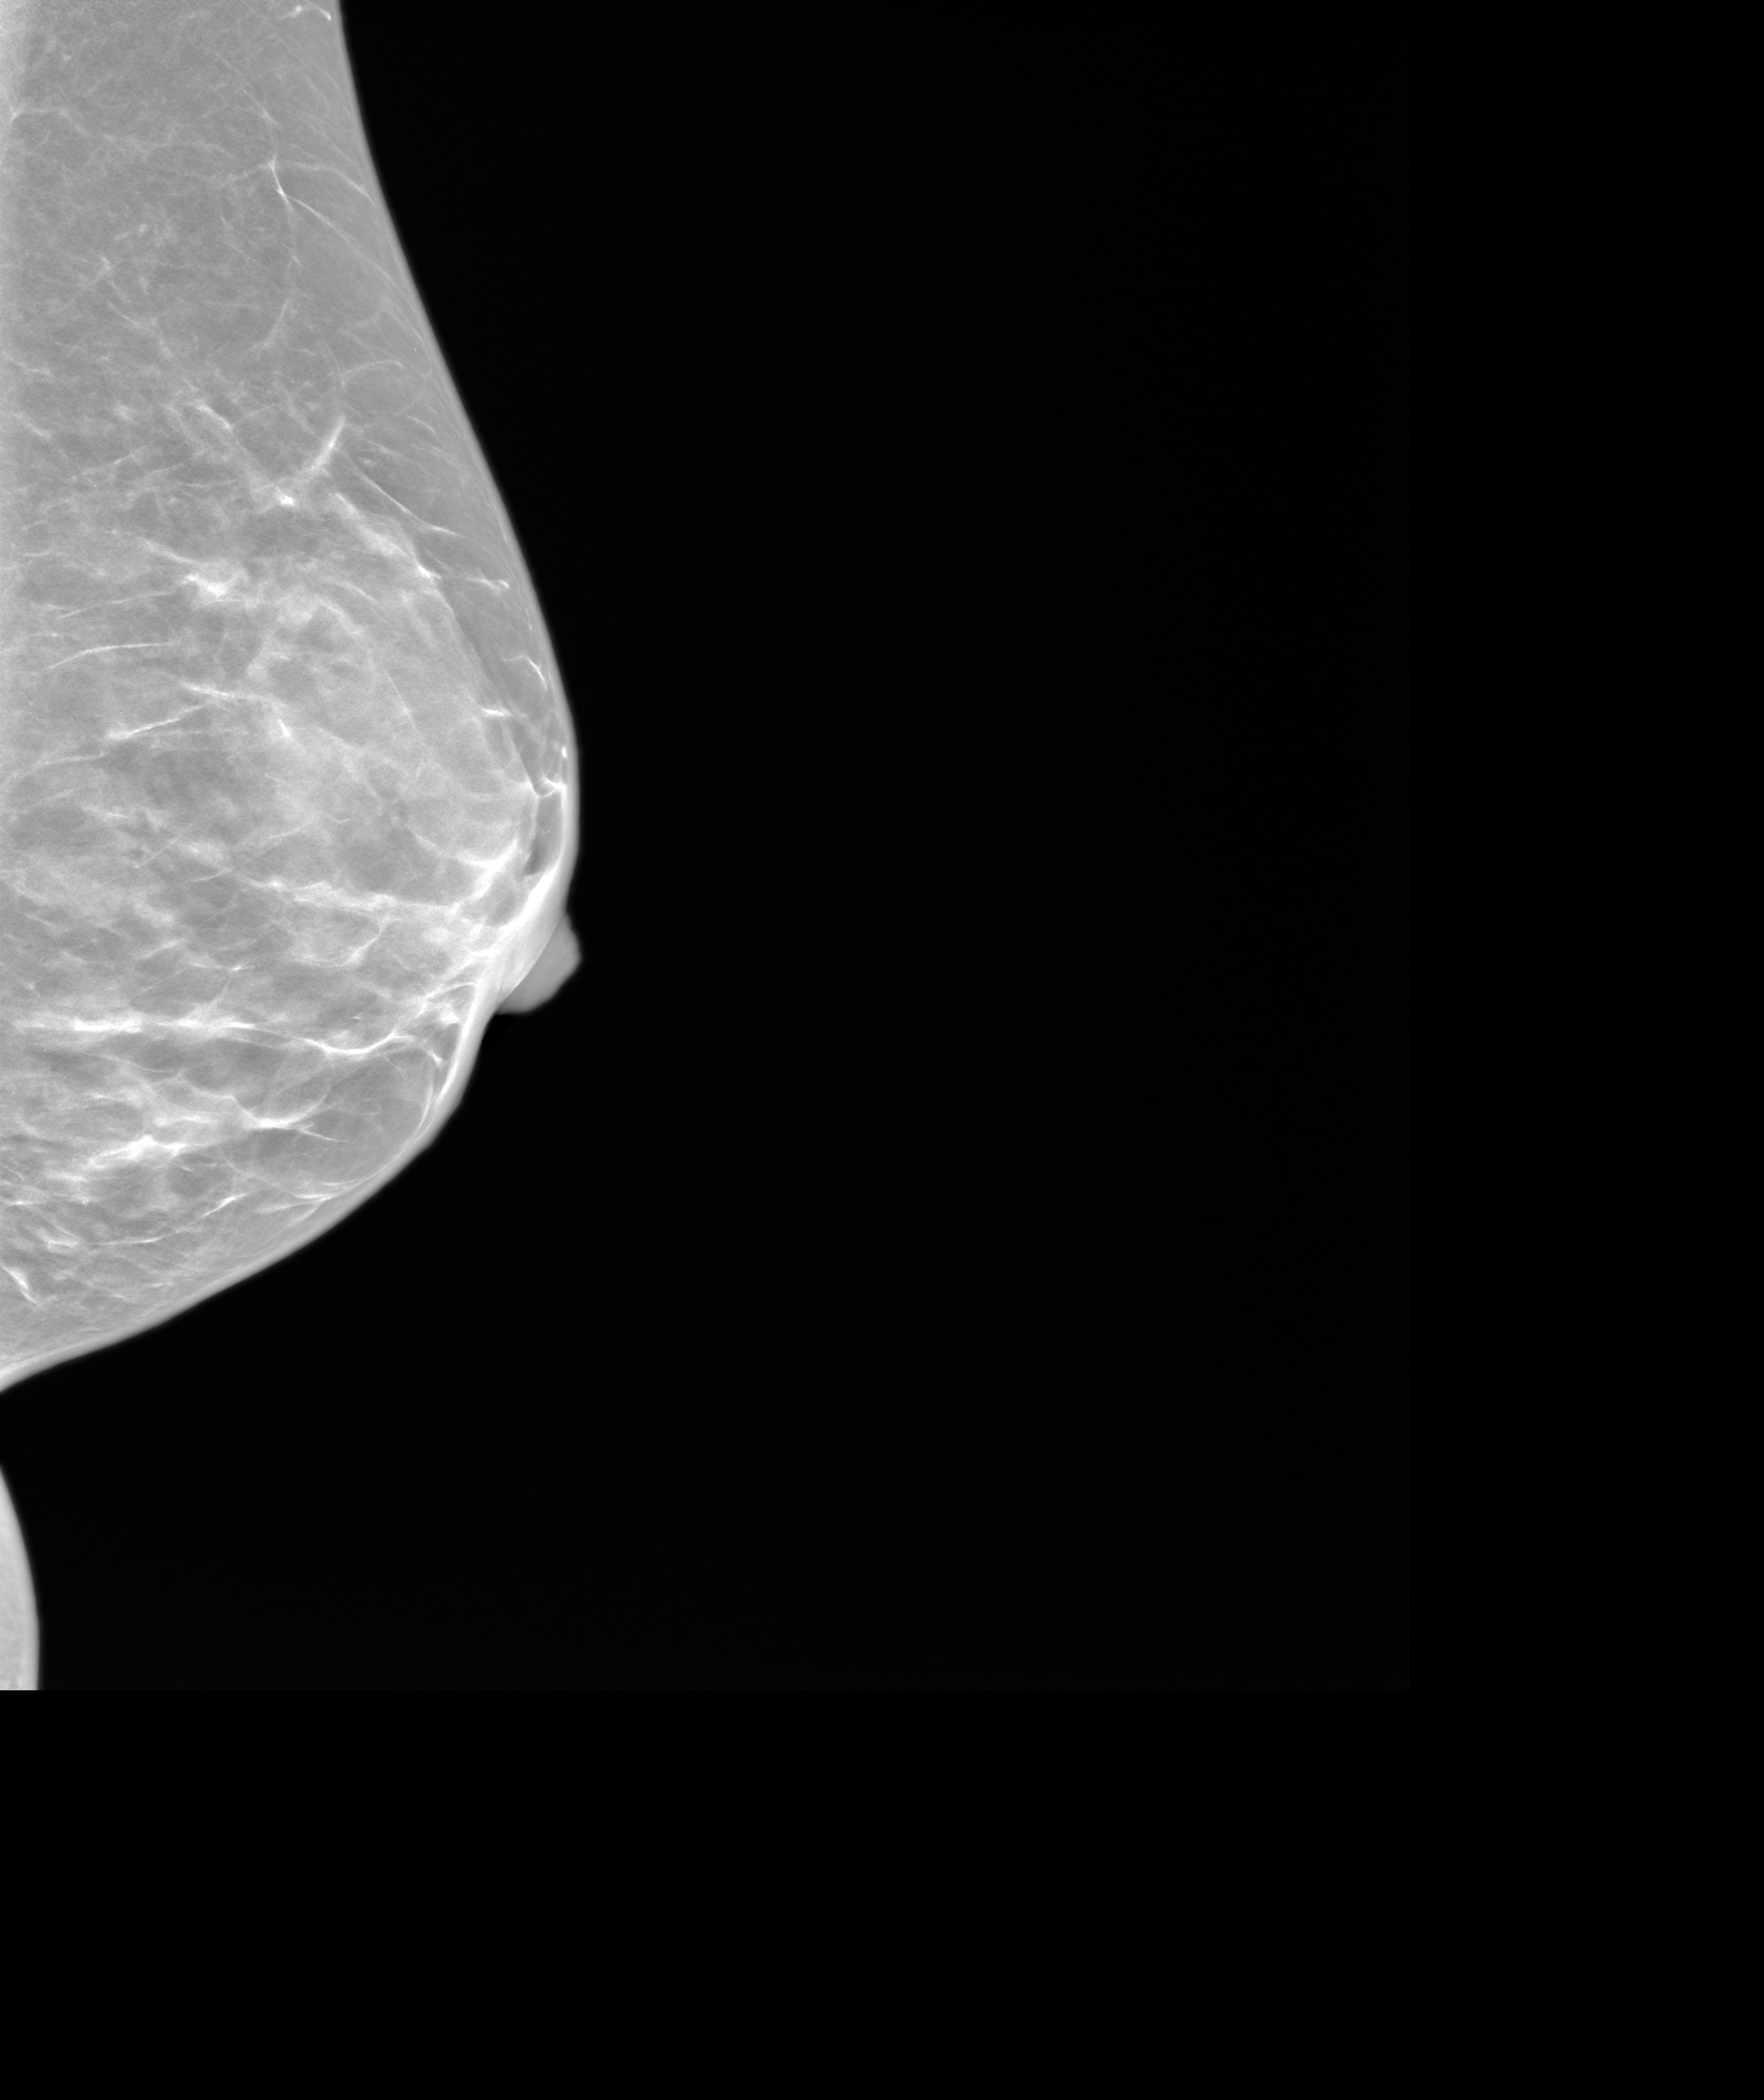
Diagnostic work-up study; system: SenoIris_1SP1.2(425). Patient aged 49 years (female).
Image type: synthesized 2-D view from tomosynthesis. Breast: left. Projection: LM view.